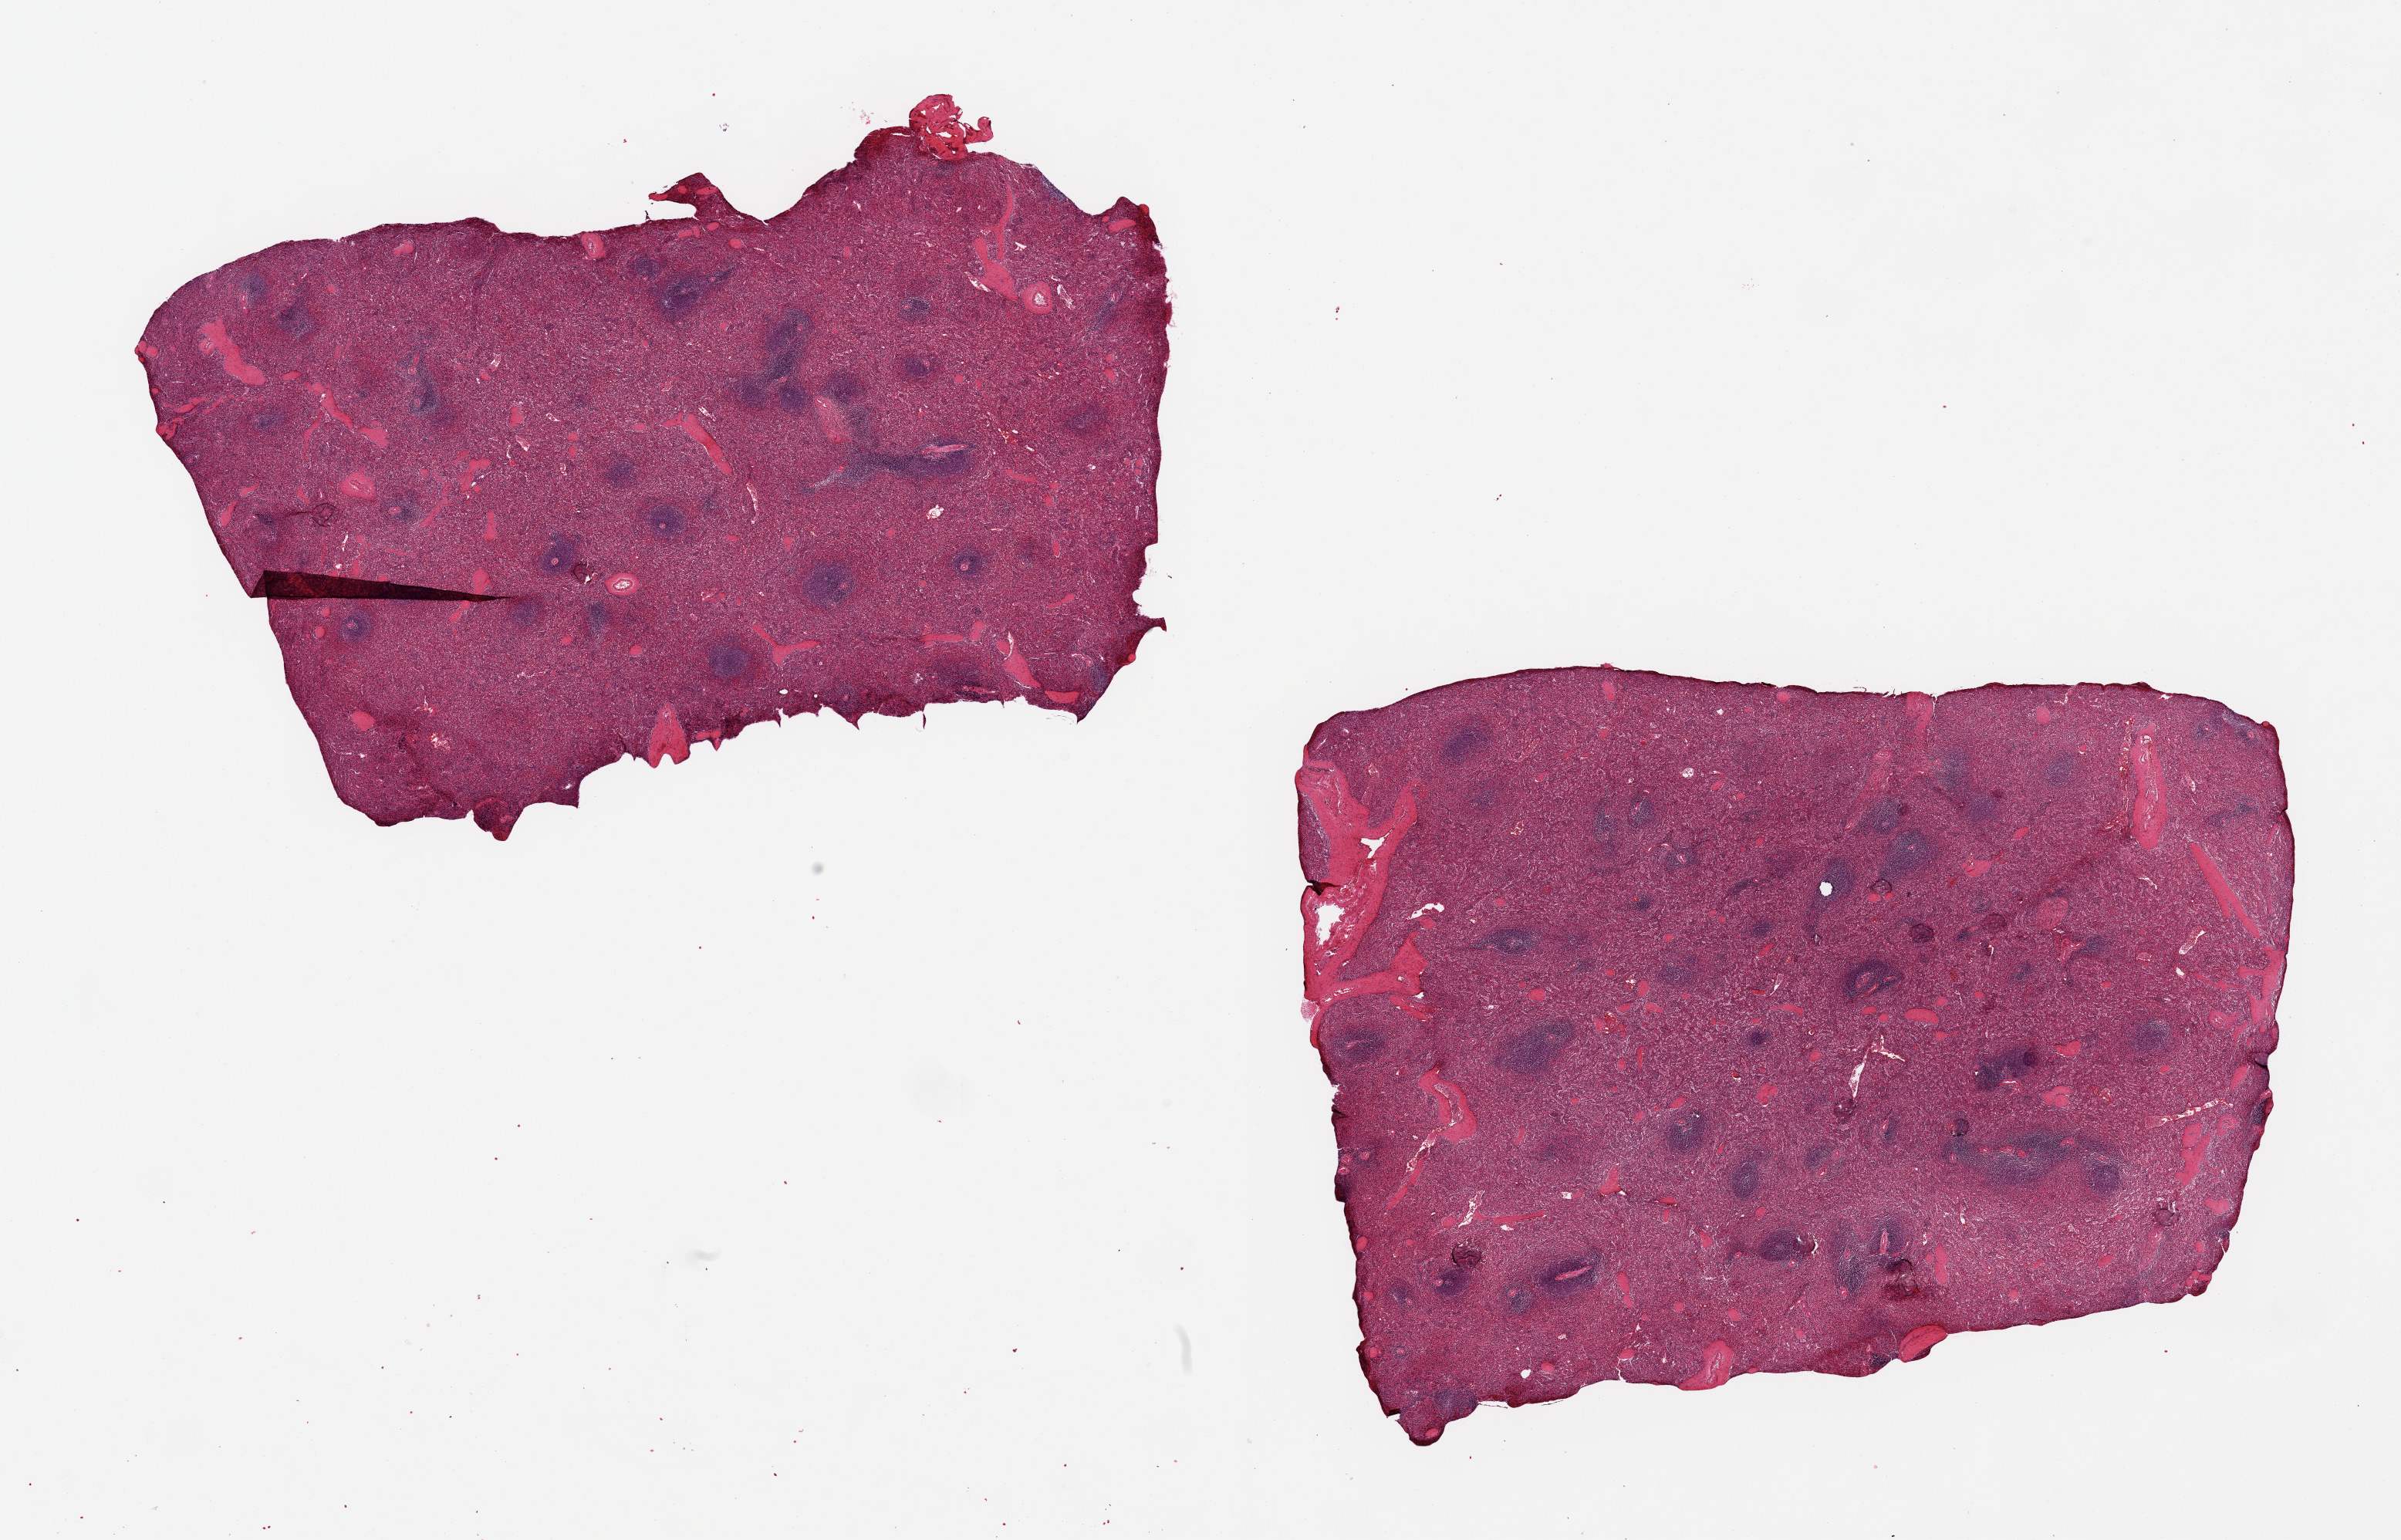
Digitized H&E-stained section — low-resolution overview of the scanned area, about 24.6 x 15.8 mm; PAXgene-fixed, paraffin-embedded tissue; section of spleen (target tissue); donor tissue sample. Donor: female.
Pathologist's review note for this sample: 2 pieces 10x7 & 10x6 mm; slight congestion.